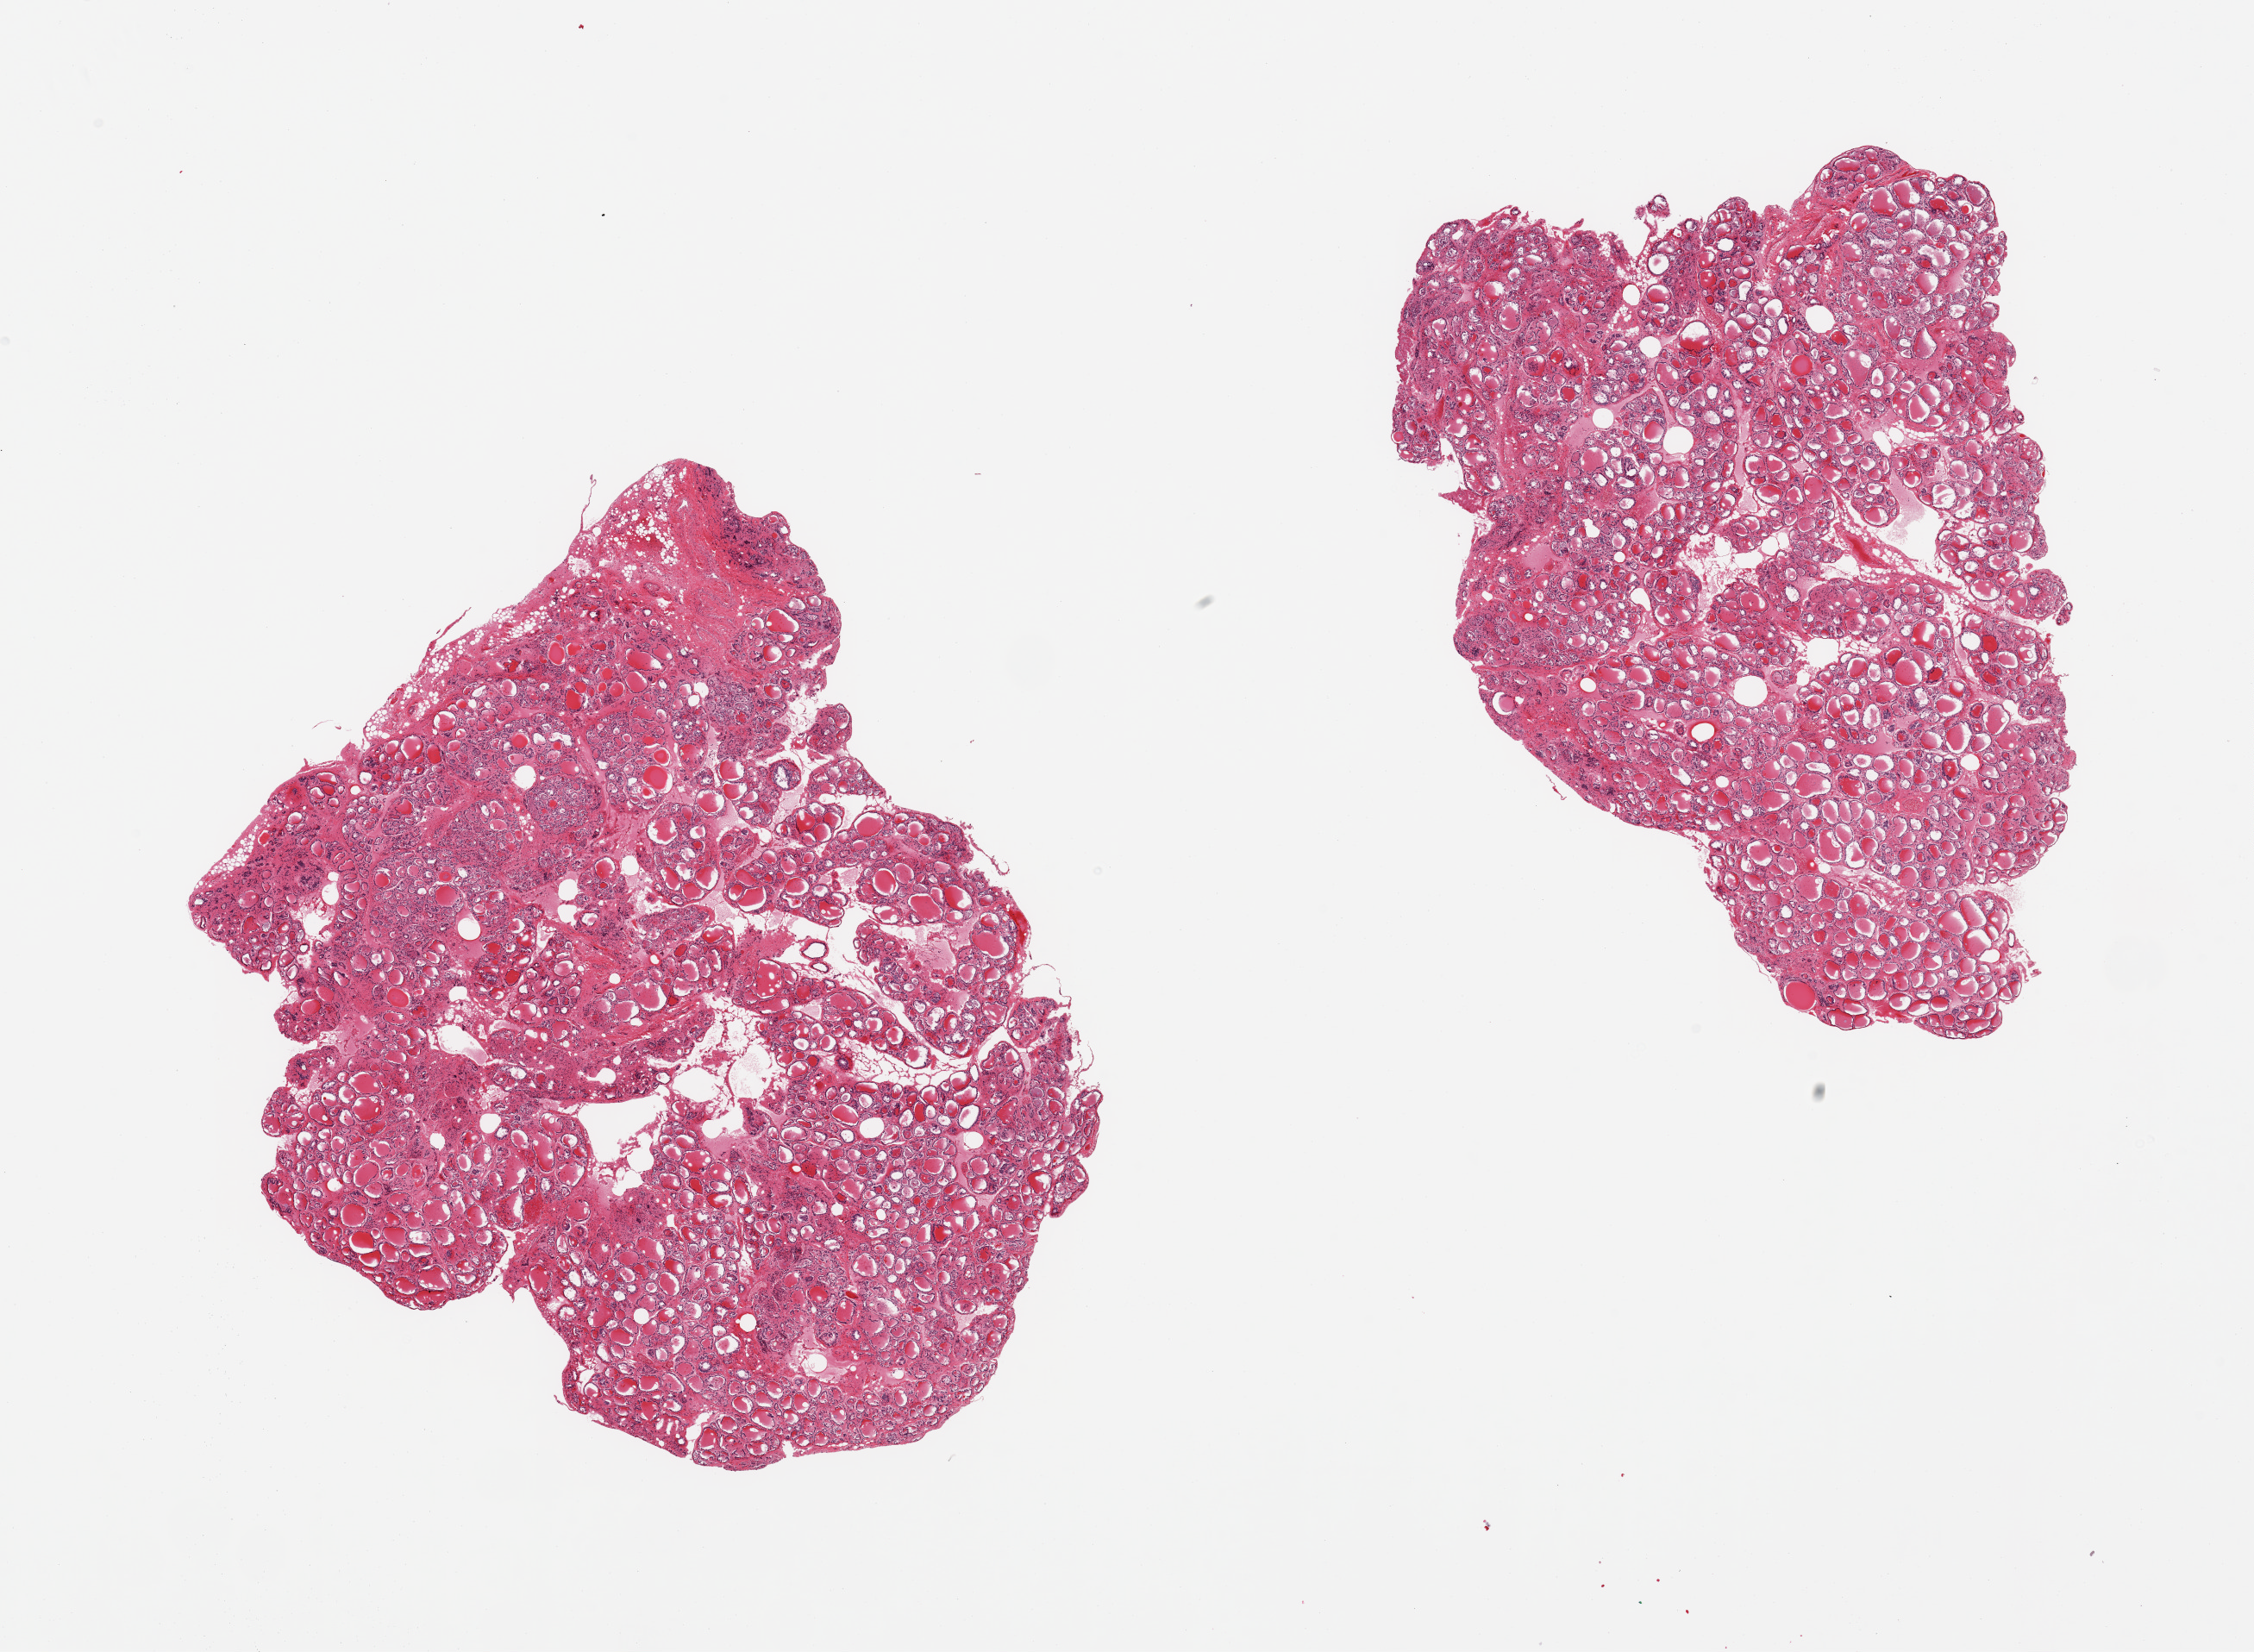
Haematoxylin and eosin whole-slide image, brightfield — low-resolution overview of the scanned area, about 20.7 x 15.2 mm. PAXgene-fixed paraffin-embedded (PFPE) section. Sampled site (target tissue): thyroid. Donor tissue sample.
Reviewer comment on this tissue sample: 2 pieces.